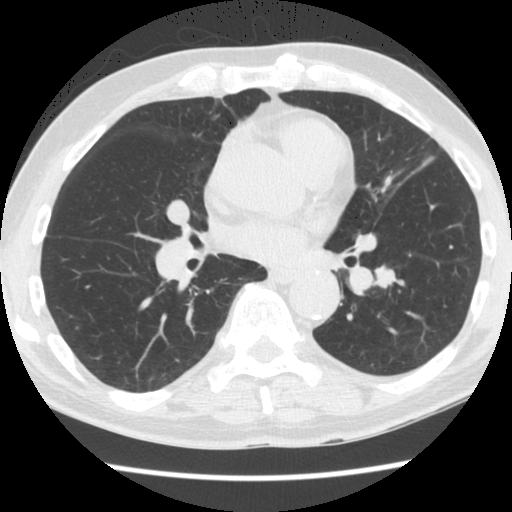
Low-dose screening chest CT, one axial slice; slice 79 of 174 in the series (ordered by position); reconstruction kernel STANDARD; lung window (W 1500 / L -600 HU); 2.5 mm slice thickness; 512 × 512 image matrix, field of view 320 × 320 mm.
Annotated regions visible in this slice (expert manual segmentation):
- lesion 1 (tumor, lower lobe of left lung): bounding box (x1, y1, x2, y2) in pixels: (376, 268, 395, 287)